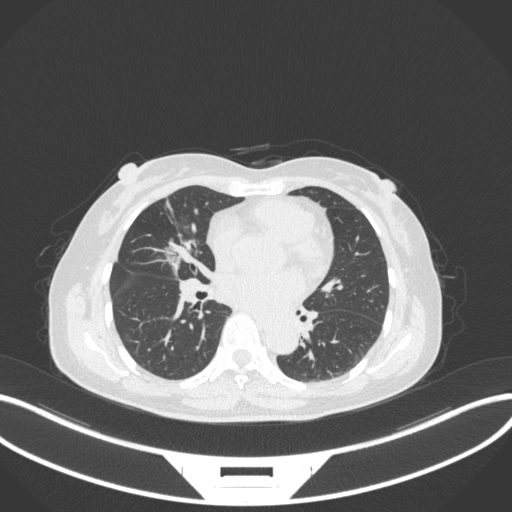
Chest CT, one axial slice. Position 142 of 282 along the scan axis. 120 kVp. Lung window (W 1500 / L -600 HU). 1 mm slice thickness. 512 × 512 image matrix, field of view 400 × 400 mm. Patient: female, 51 years. From the clinical record (not read from this slice): clinical TNM (as recorded): T1c N0 M0; histopathological grade: G2.
Structures marked on this image (rectangle marked by the reading radiologist):
- lung tumour (recorded histology: adenocarcinoma): bounding box <154,227,196,277> (left, top, right, bottom; pixels)